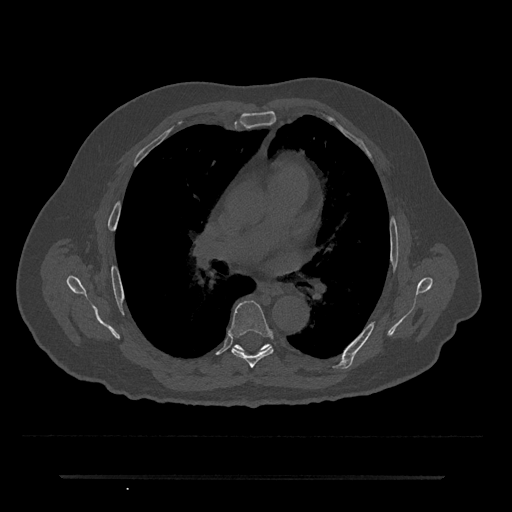
CT including the spine, one axial slice; slice 425 of 797 in the series (ordered by position); 120 kVp; bone window (W 1800 / L 400 HU); 0.5 mm slice thickness; 512 × 512 image matrix. Patient: male, 69 years. Case-level facts recorded for this patient, not image findings: primary cancer: prostate.
Outlined on this slice (semi-automatic segmentation, software-assisted and operator-edited):
- T6 vertebra: box from (x=229, y=301) to (x=273, y=368) px
- T7 vertebra: (x=235, y=345)–(x=241, y=349)